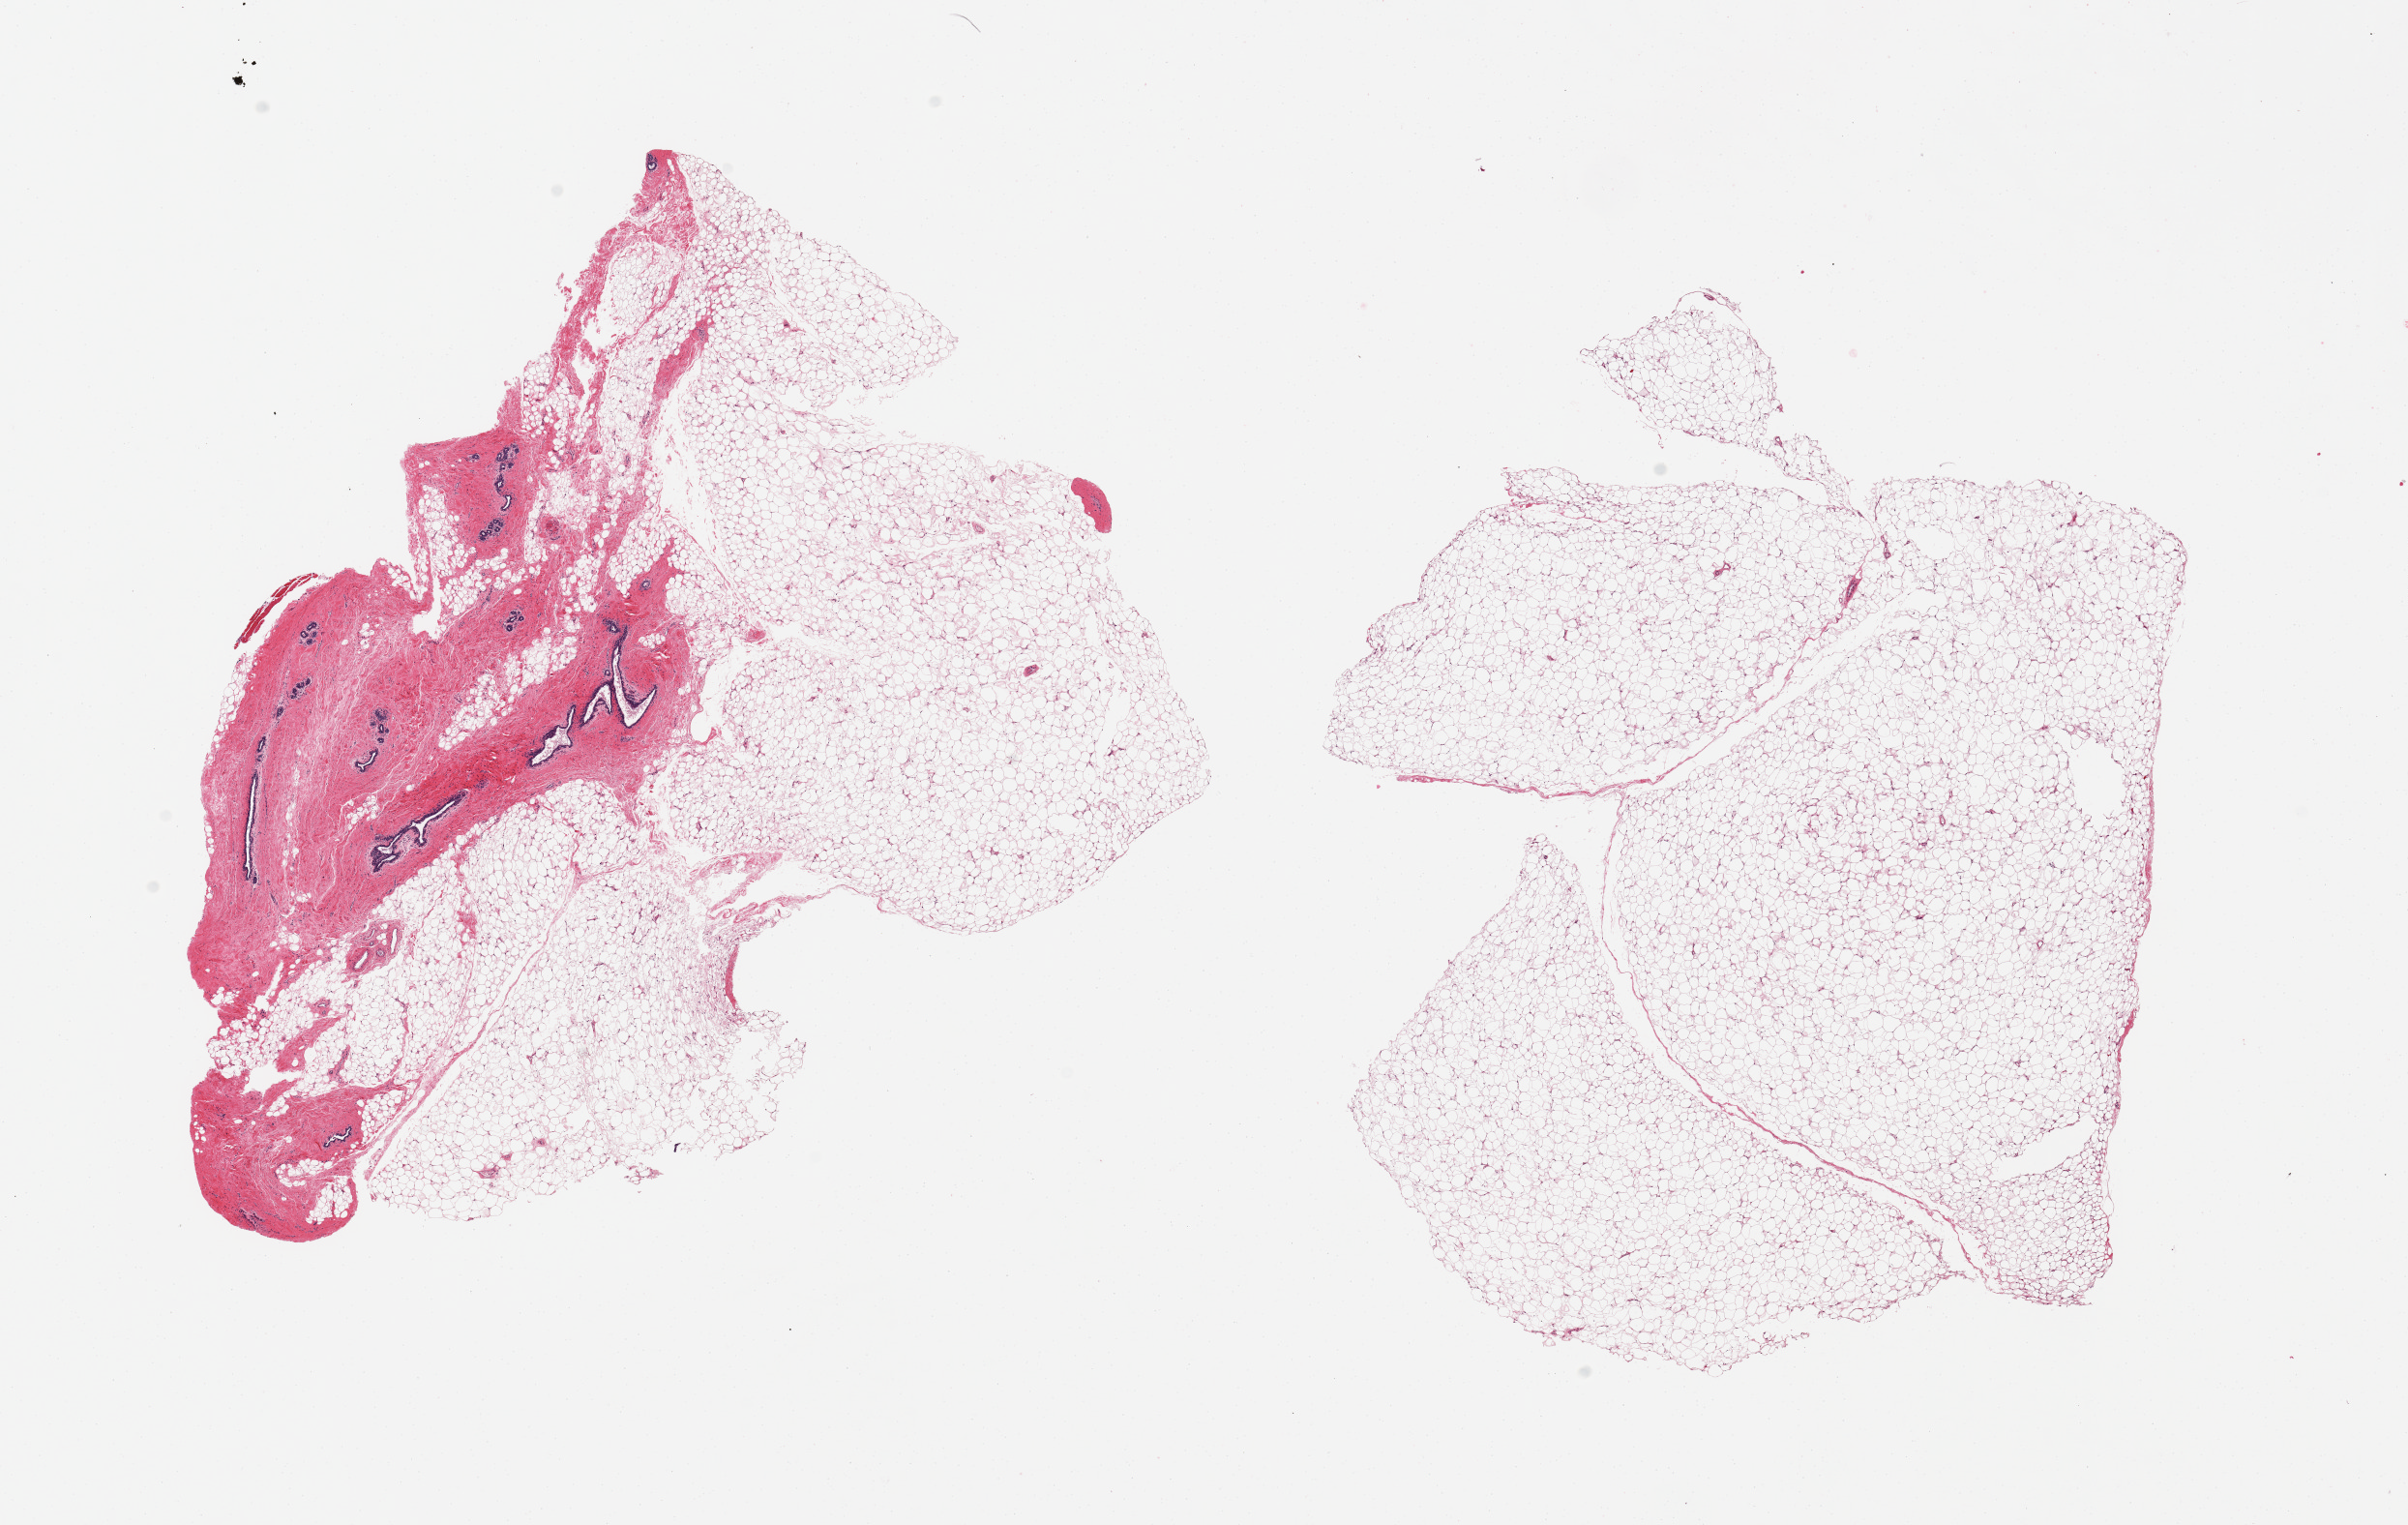
Hematoxylin and eosin (H&E) whole-slide image — whole scanned area (about 19.7 x 12.5 mm, acquisition: 20x scan) shown as a low-resolution overview; PAXgene-fixed, paraffin-embedded tissue; sampled site (target tissue): breast; donor tissue sample. Male donor.
Review note (as recorded): 2 pieces, mainly fibroadipose elements, focal stromal and ductal gynecomastoid hyperplasia.